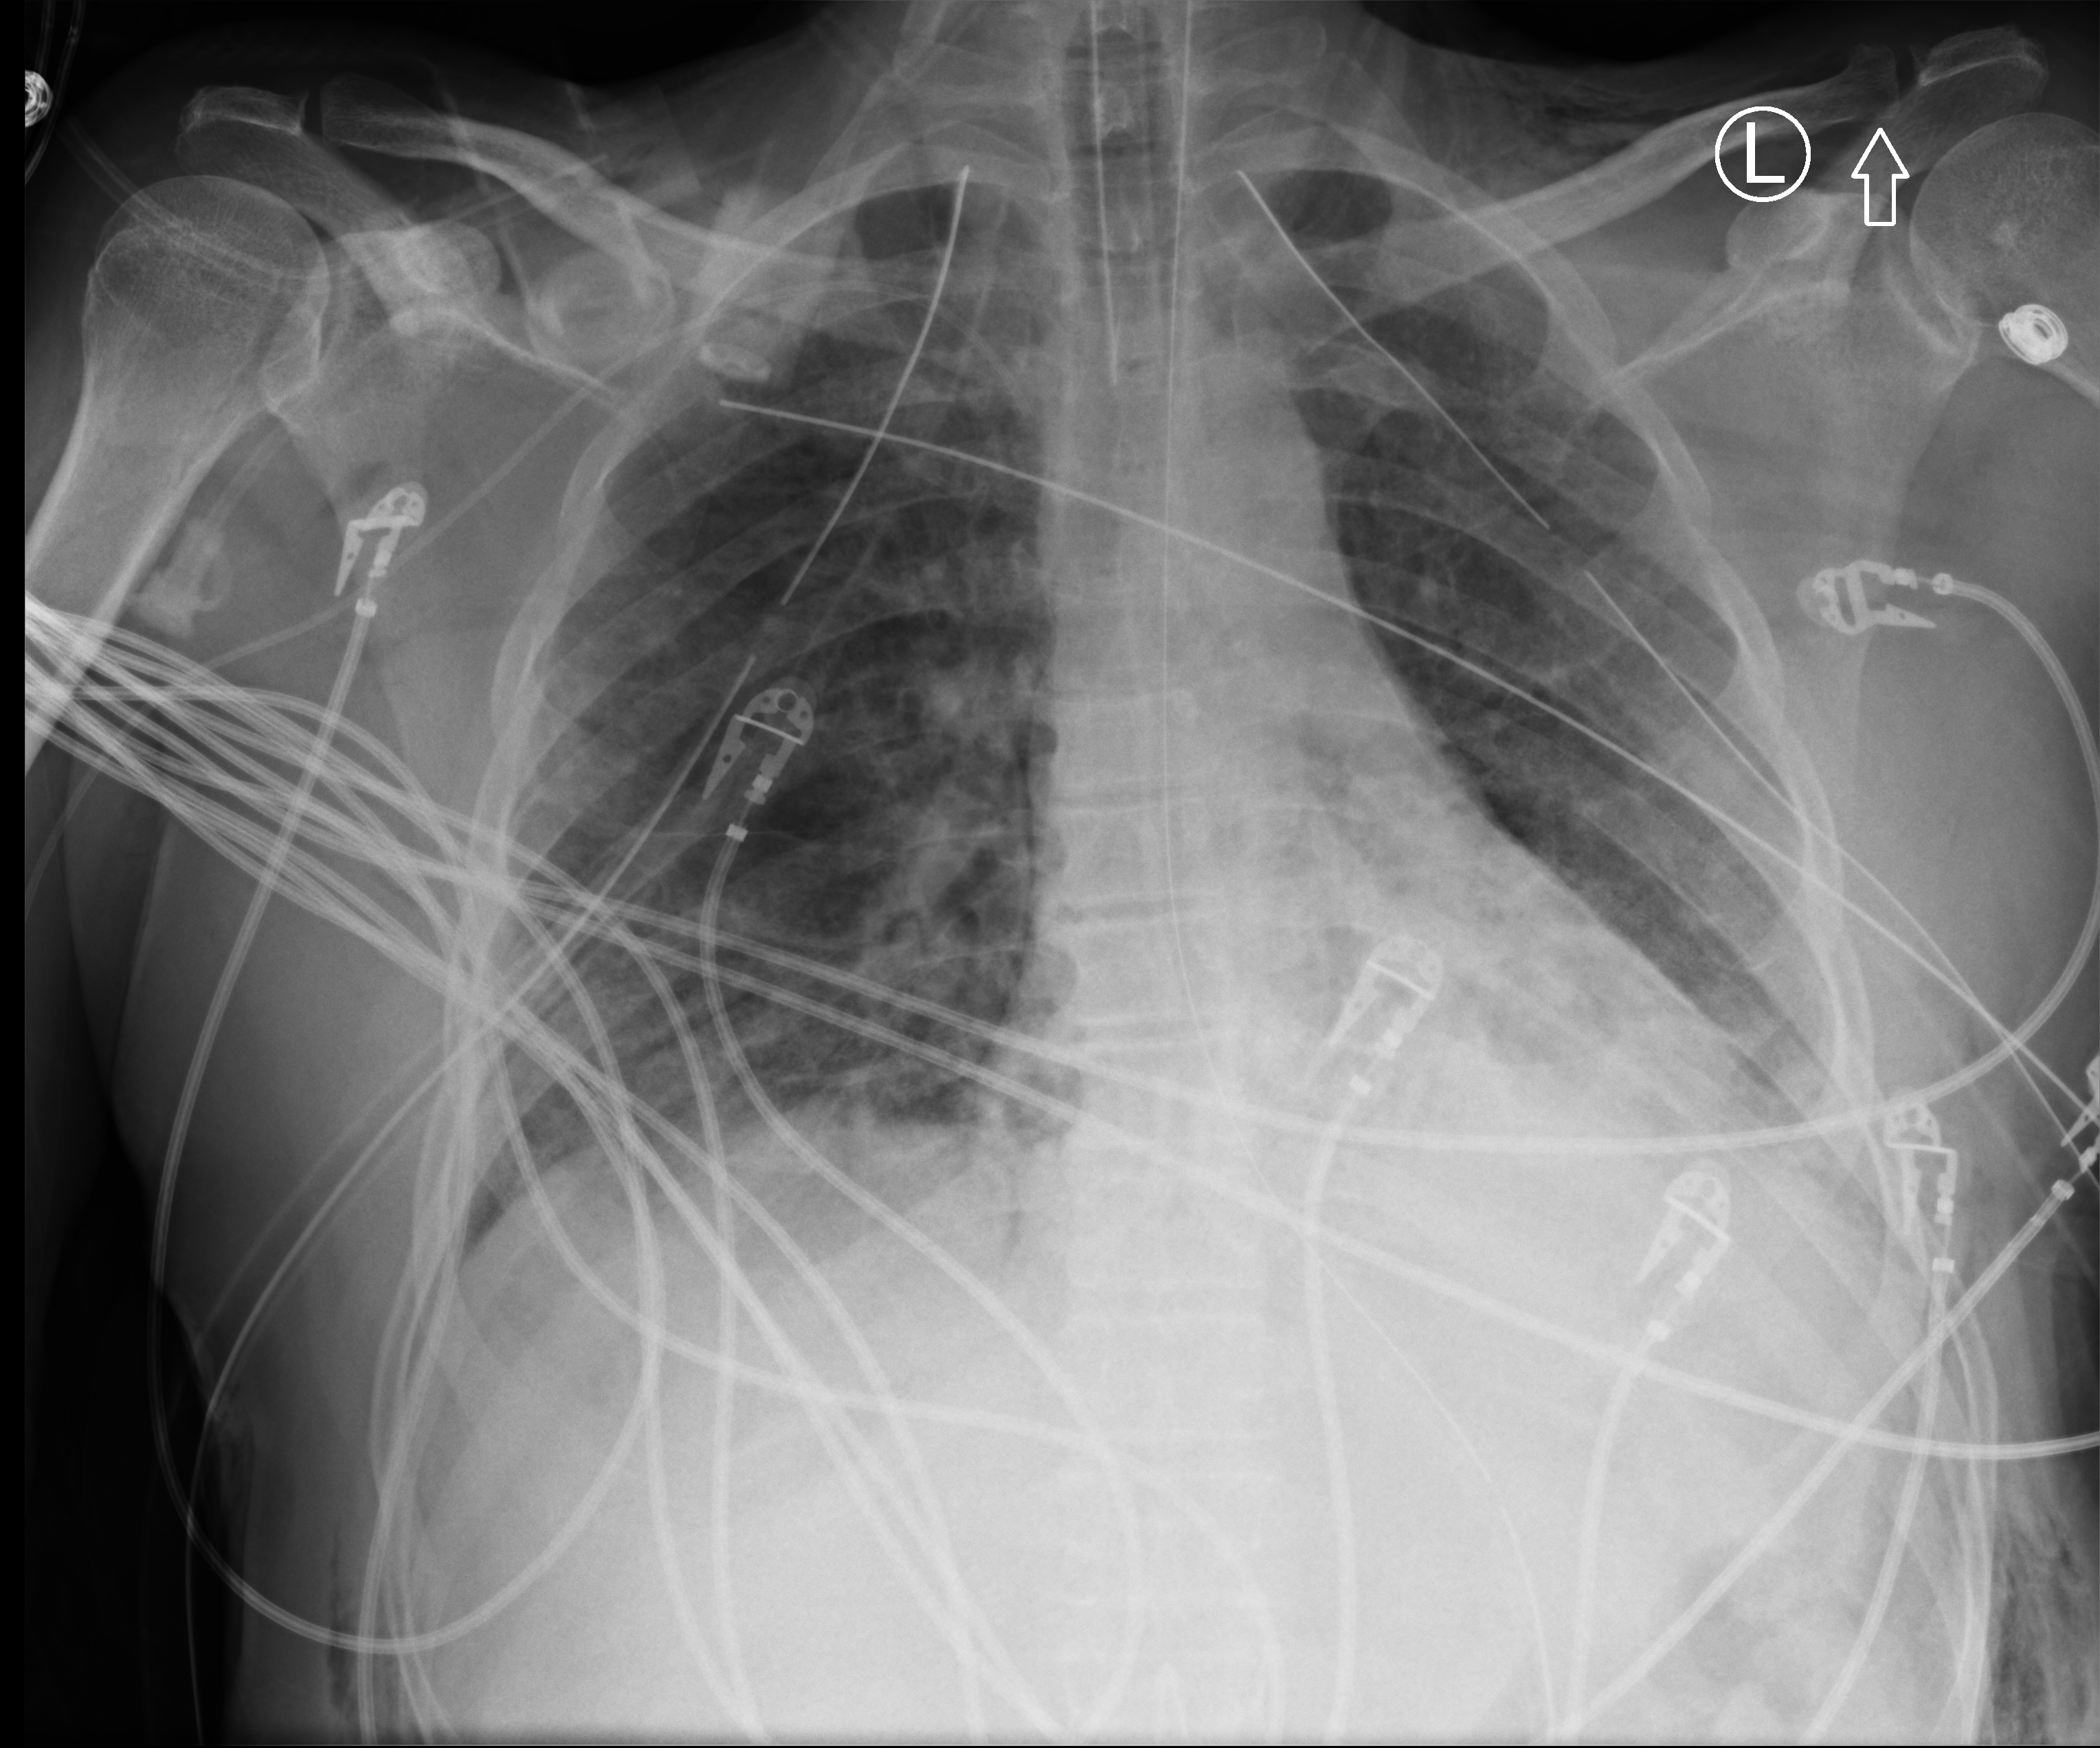
Chest X-ray (portable), anteroposterior (AP) projection. Male patient hospitalised with COVID-19, age 18–59 years.
Hospital-stay facts (about this admission, not read from this image; timing relative to this image not recorded): admitted to intensive care during this hospital stay: yes; mechanically ventilated during this hospital stay: yes; hypertension (admission record): yes.